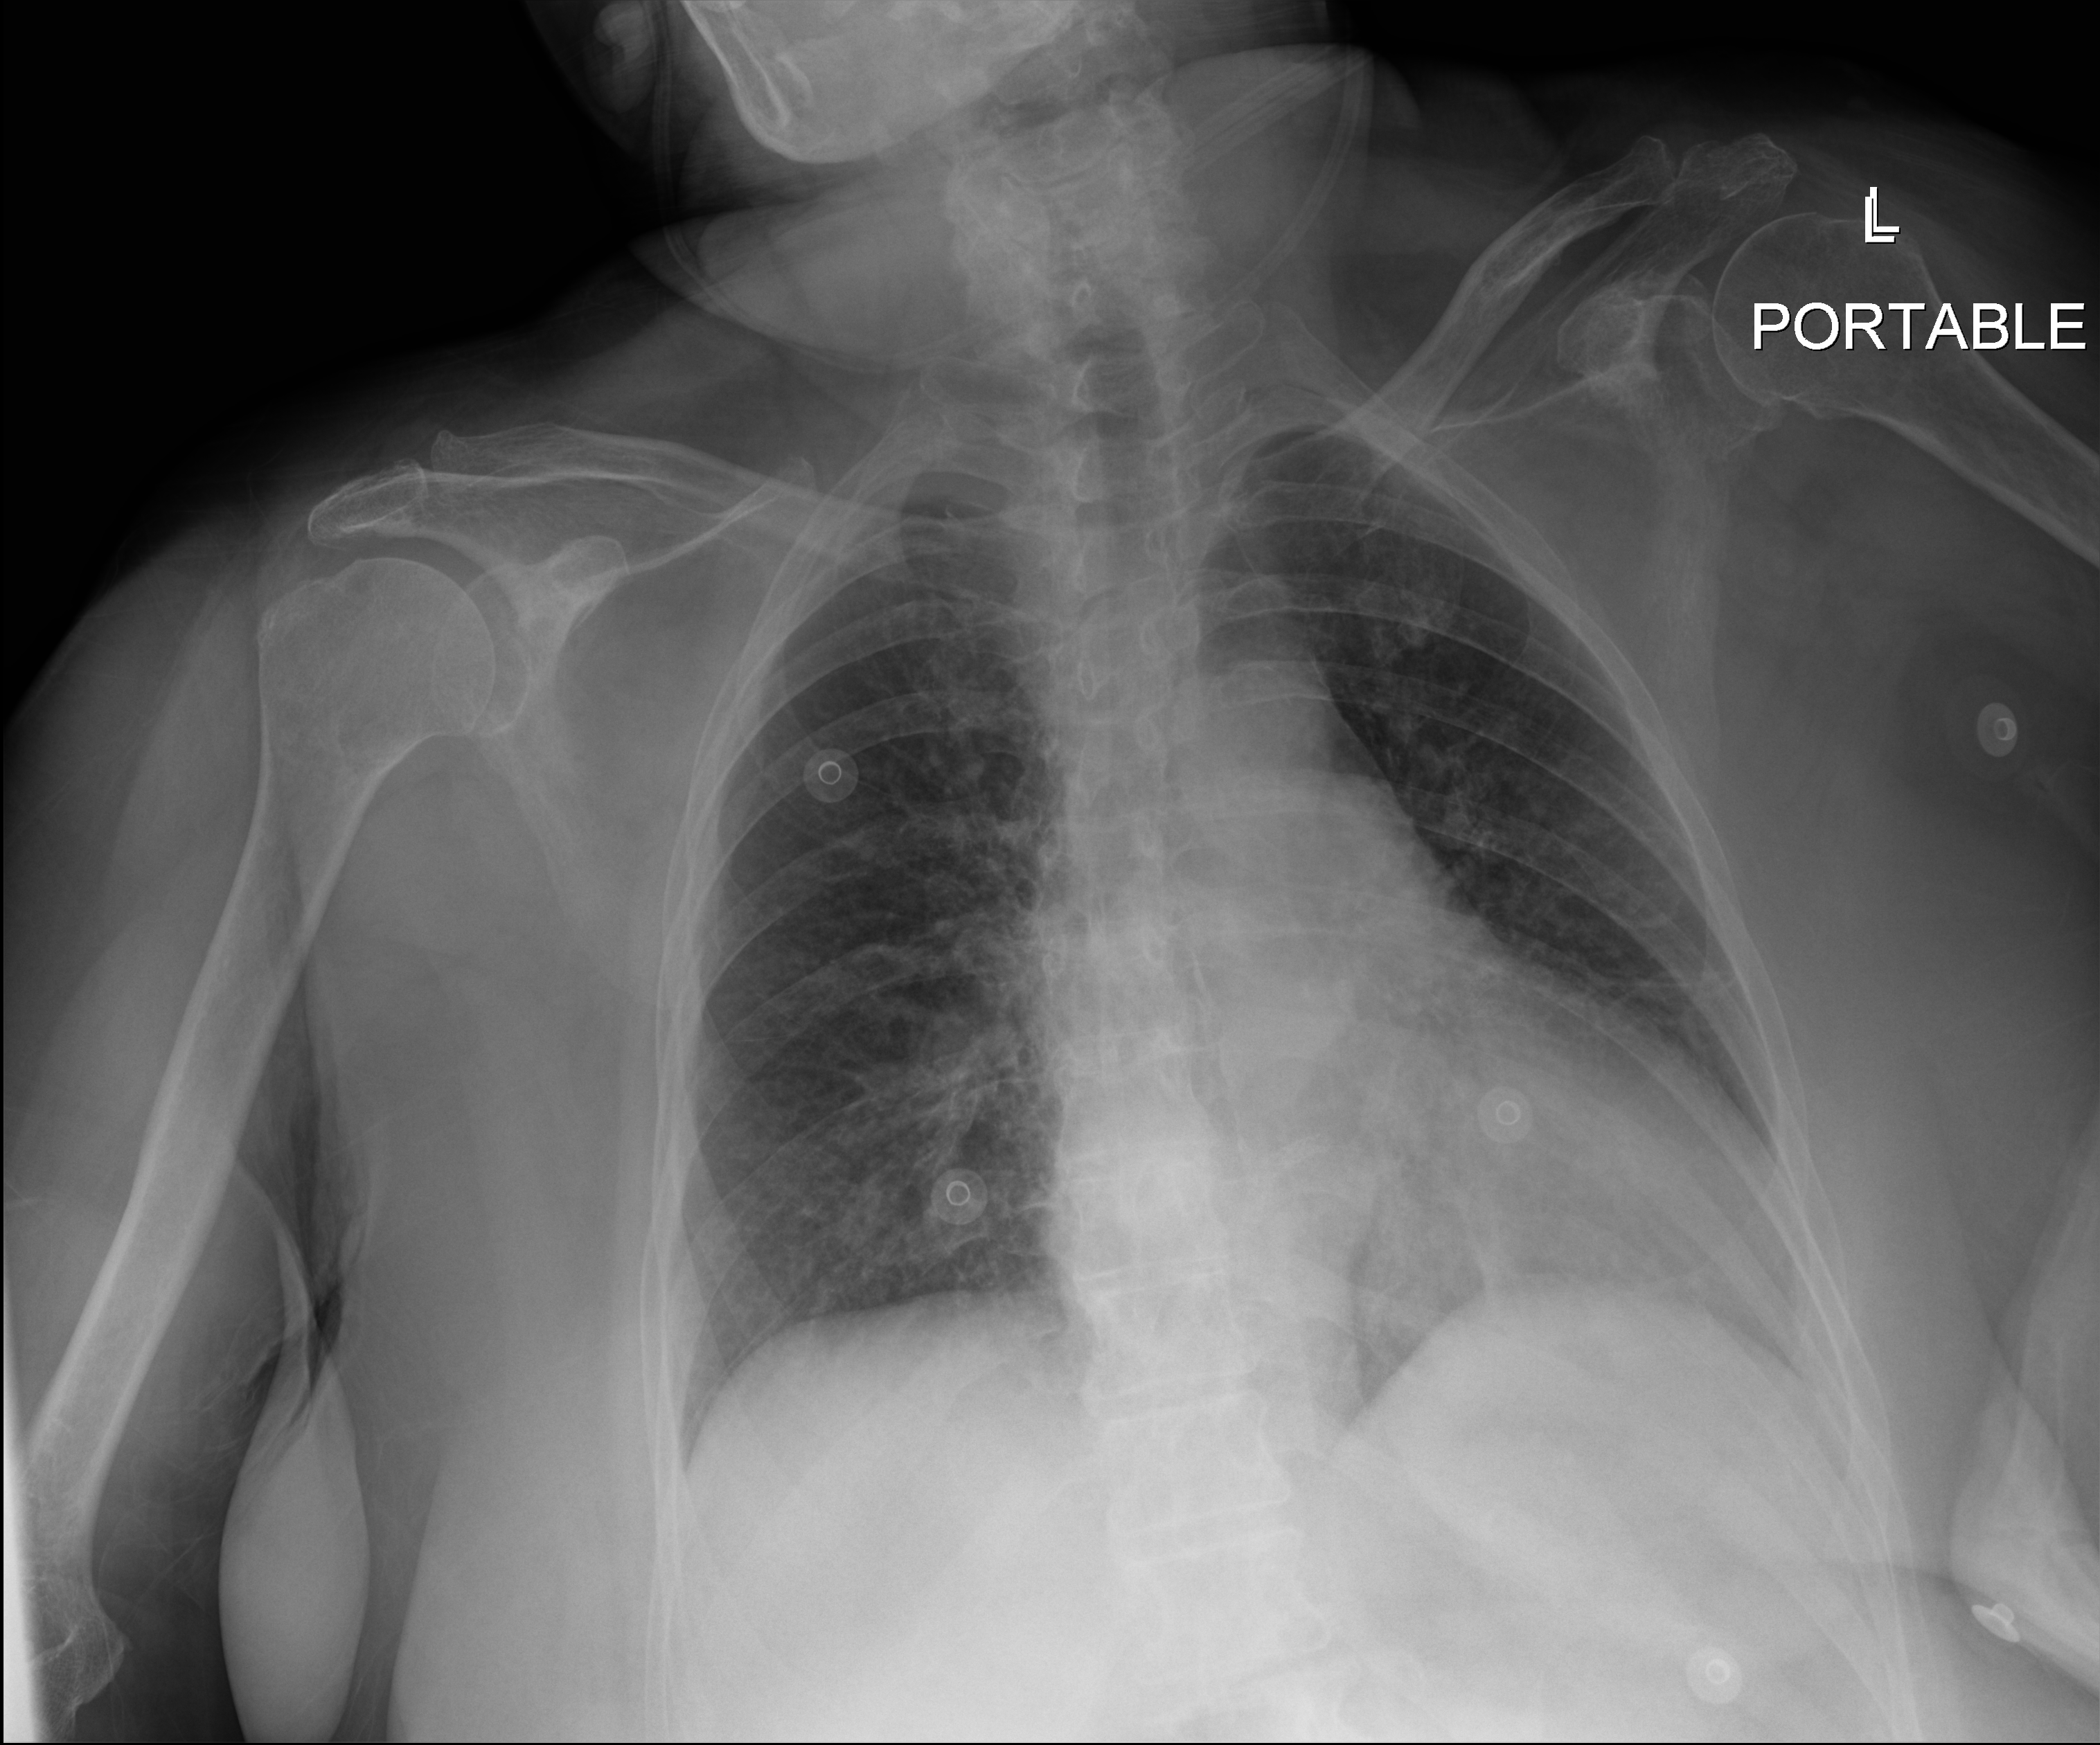
Chest radiograph (digital radiography); anteroposterior (AP) projection. Patient hospitalised with COVID-19; female, aged 75–90 years.
From the hospital-stay record, not from the radiograph (when in the stay this image was taken is not recorded):
- mechanically ventilated during this hospital stay: no
- admitted to intensive care during this hospital stay: no